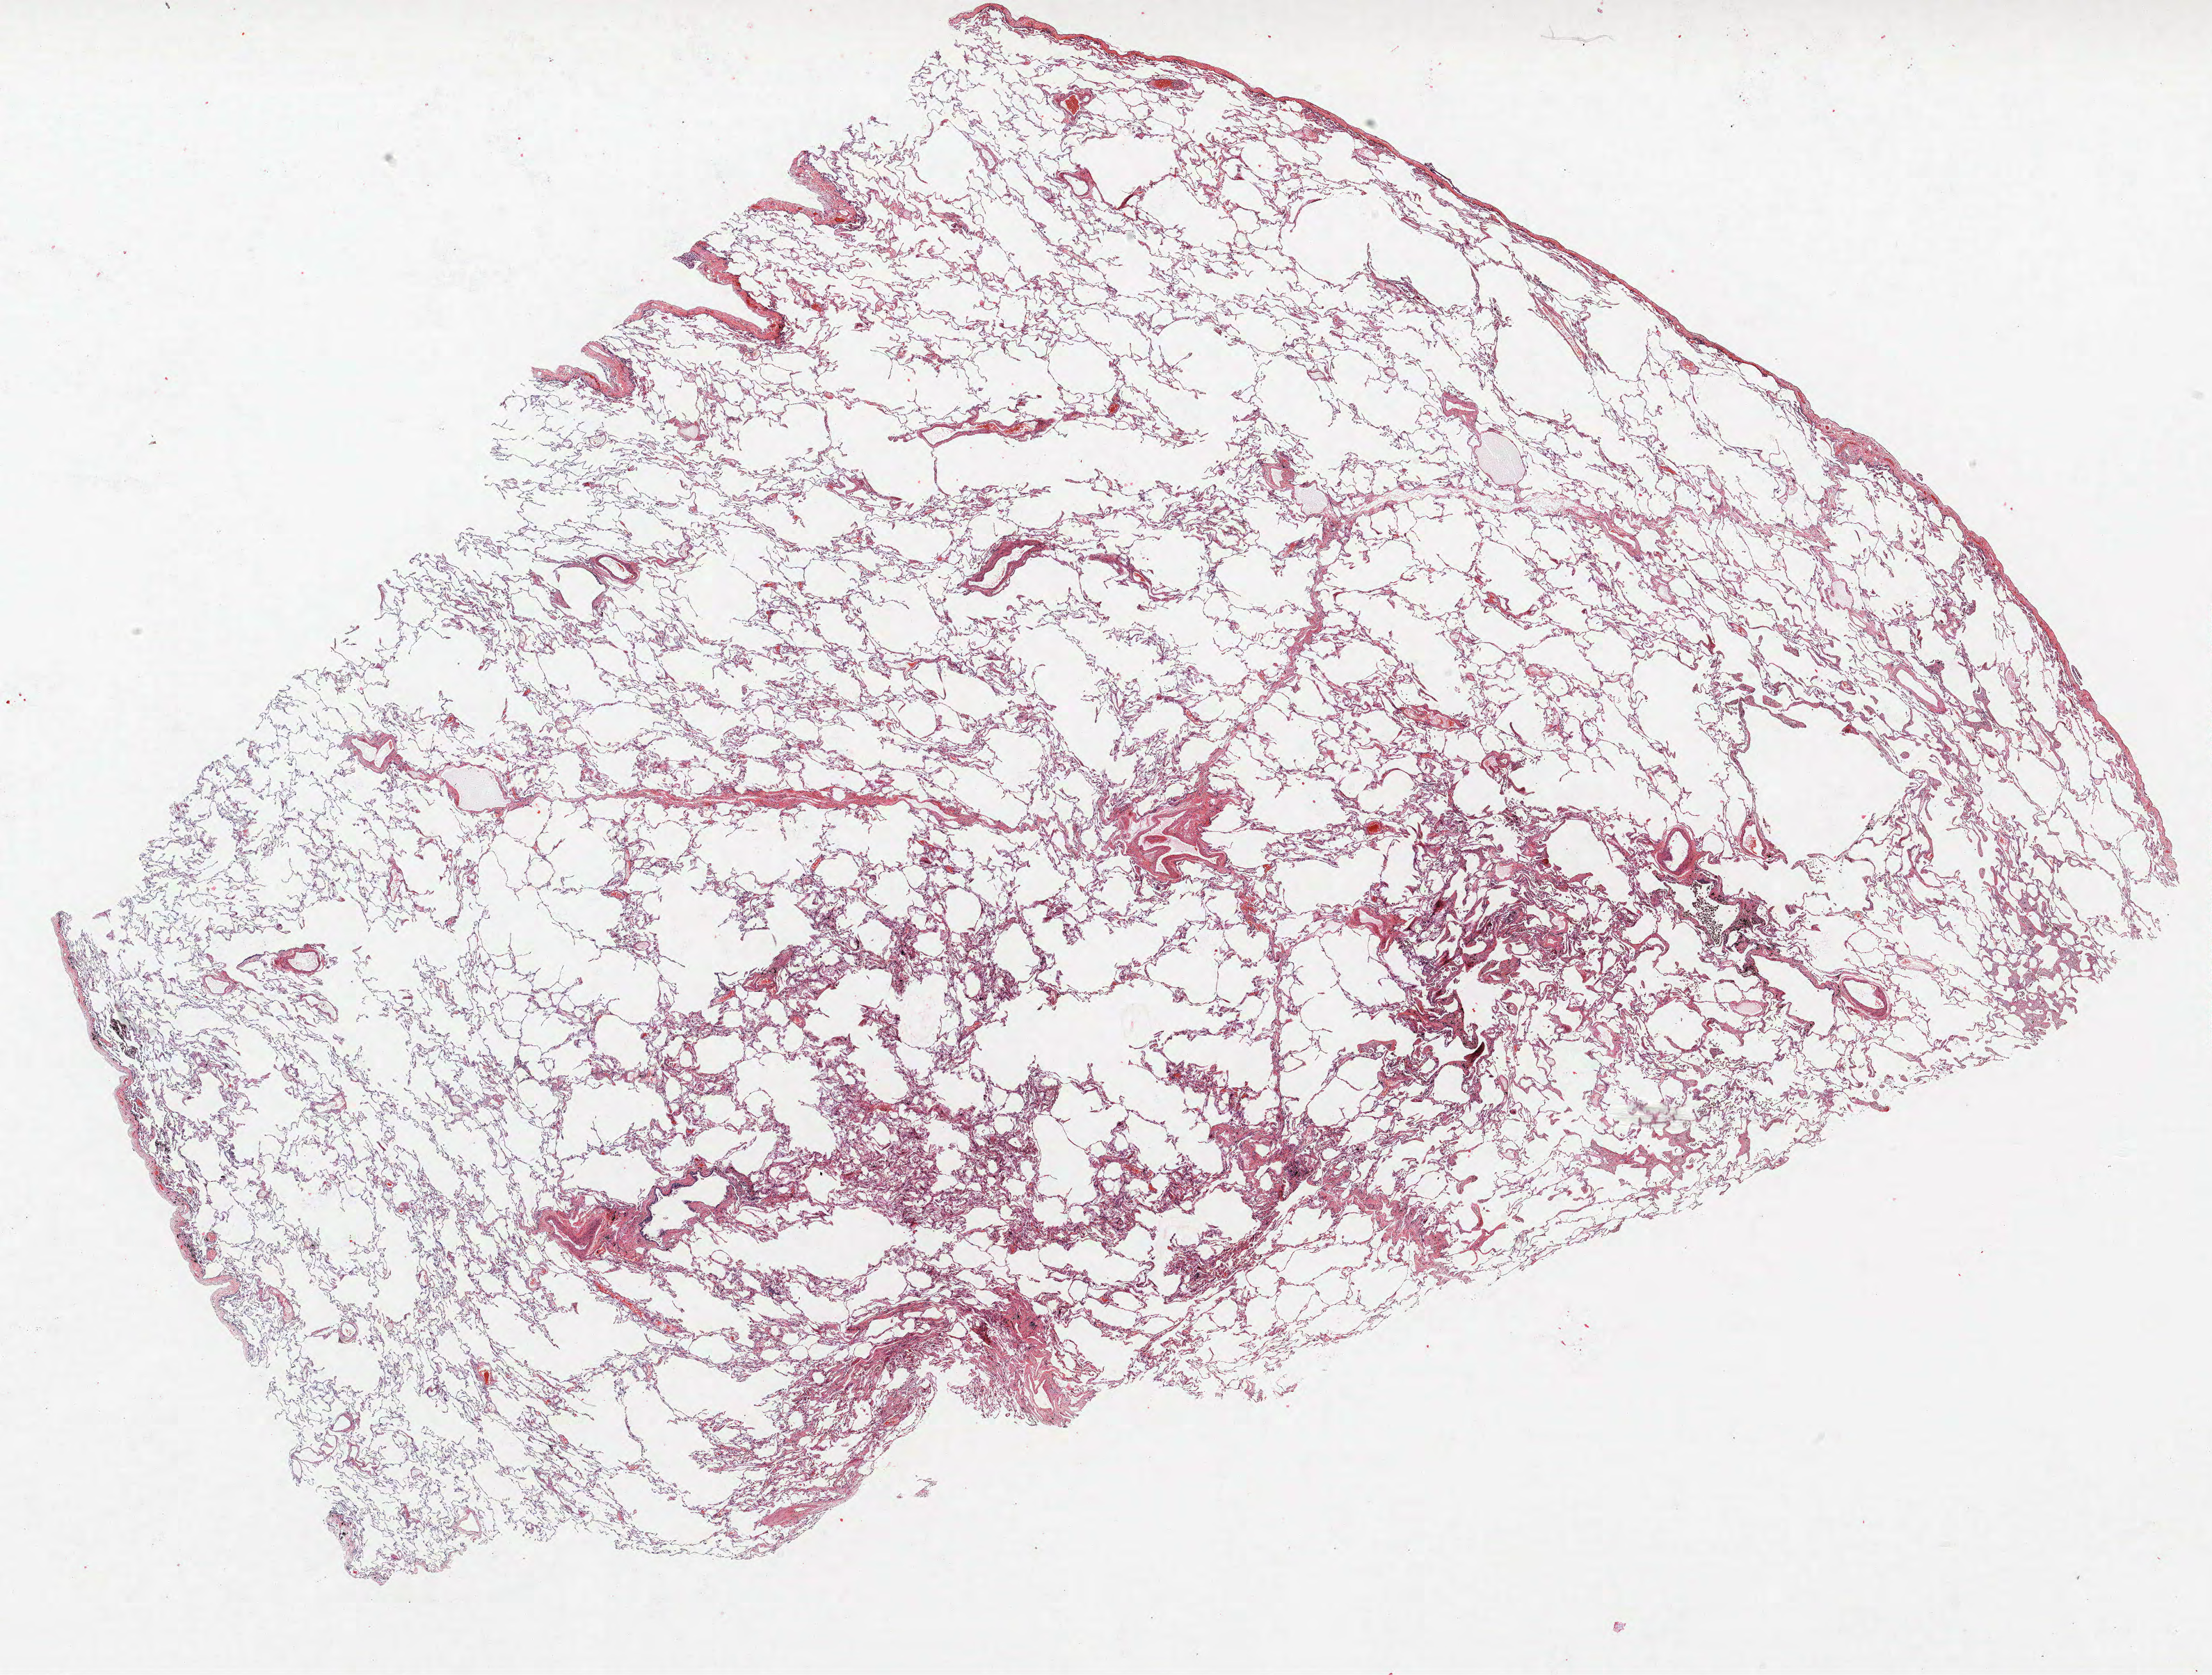
H&E-stained whole-slide image, low-resolution overview of the scanned area, about 25.4 x 19.3 mm, FFPE section, lung tissue. Male patient, aged 60 at enrolment. Grade: moderately differentiated (G2).
Tumour size (pathology): 35 mm. Stage (AJCC 6th edition): IB. Primary tumour location (clinical record): left upper lobe. Participant's lung-cancer diagnosis: Adenocarcinoma, NOS.